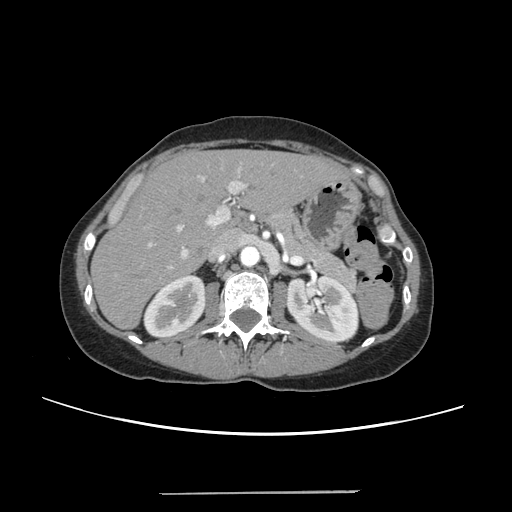
Contrast-enhanced abdominal CT, one axial slice. Position 144 of 240 along the scan axis. 120 kVp. Soft-tissue window (W 400 / L 40 HU). 1.25 mm slice thickness. 512 × 512 image matrix. Female patient, age 60 years. Case-level facts recorded for this patient, not image findings: diagnosis: colorectal cancer liver metastases, imaged before liver resection; multiple liver metastases: no; largest metastasis: 1.5 cm; disease in both lobes: no.
Outlined on this slice (manually delineated by an expert):
- liver: bounding box (x1, y1, x2, y2) in pixels: (94, 151, 344, 327)
- planned liver remnant (the part of the liver to remain after resection): (94, 151, 344, 327)
- portal vein (with intrahepatic branches): (144, 163, 252, 269)